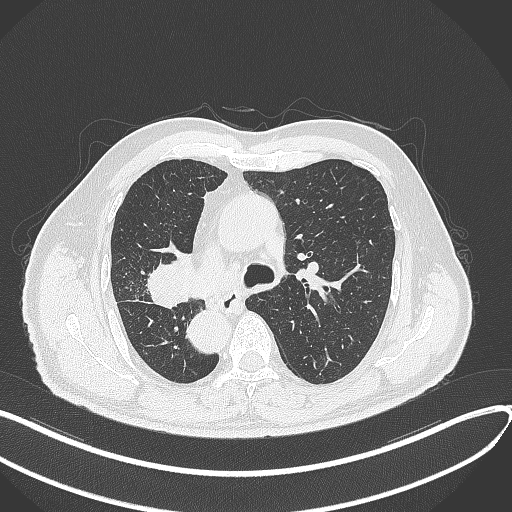
Chest CT, one axial slice. Position 202 of 300 along the scan axis. Reconstruction kernel B70f. 120 kVp. Lung window (W 1500 / L -600 HU). 512 × 512 image matrix, field of view 400 × 400 mm. Patient: male, 67 years. Case-level facts recorded for this patient, not image findings: clinical TNM (as recorded): T2a N0 M0.
Structures marked on this image (bounding box drawn by a radiologist):
- lung tumour (recorded histology: squamous cell carcinoma): box from (x=148, y=250) to (x=193, y=309) px